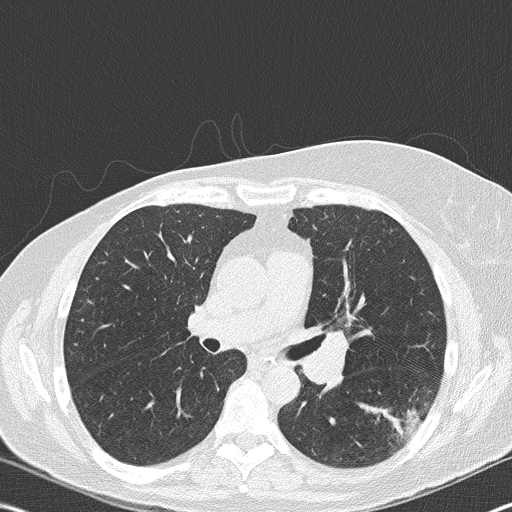
Chest CT (low-dose screening protocol), one axial image; second screening round (one year after baseline); lung window (W 1500 / L -600 HU); 2 mm slice thickness. Female participant, aged 60 years at enrolment. Current smoker at enrolment.
• Expert-annotated lung lesion, bounding box [x1, y1, x2, y2] px = [374, 382, 444, 451].
• Screening reader's record for this exam (one nodule recorded; not confirmed to be the boxed lesion): non-calcified nodule or mass ≥4 mm, left lower lobe, 18 × 16 mm, spiculated (stellate) margins, soft tissue attenuation, pre-existing on the prior screen: no.
• Official screen result: positive, other.
• Participant outcome: lung cancer diagnosed 35 days after this screen — carcinoma, NOS, left hilum, stage IV (AJCC 6th edition), 45 mm at pathology.